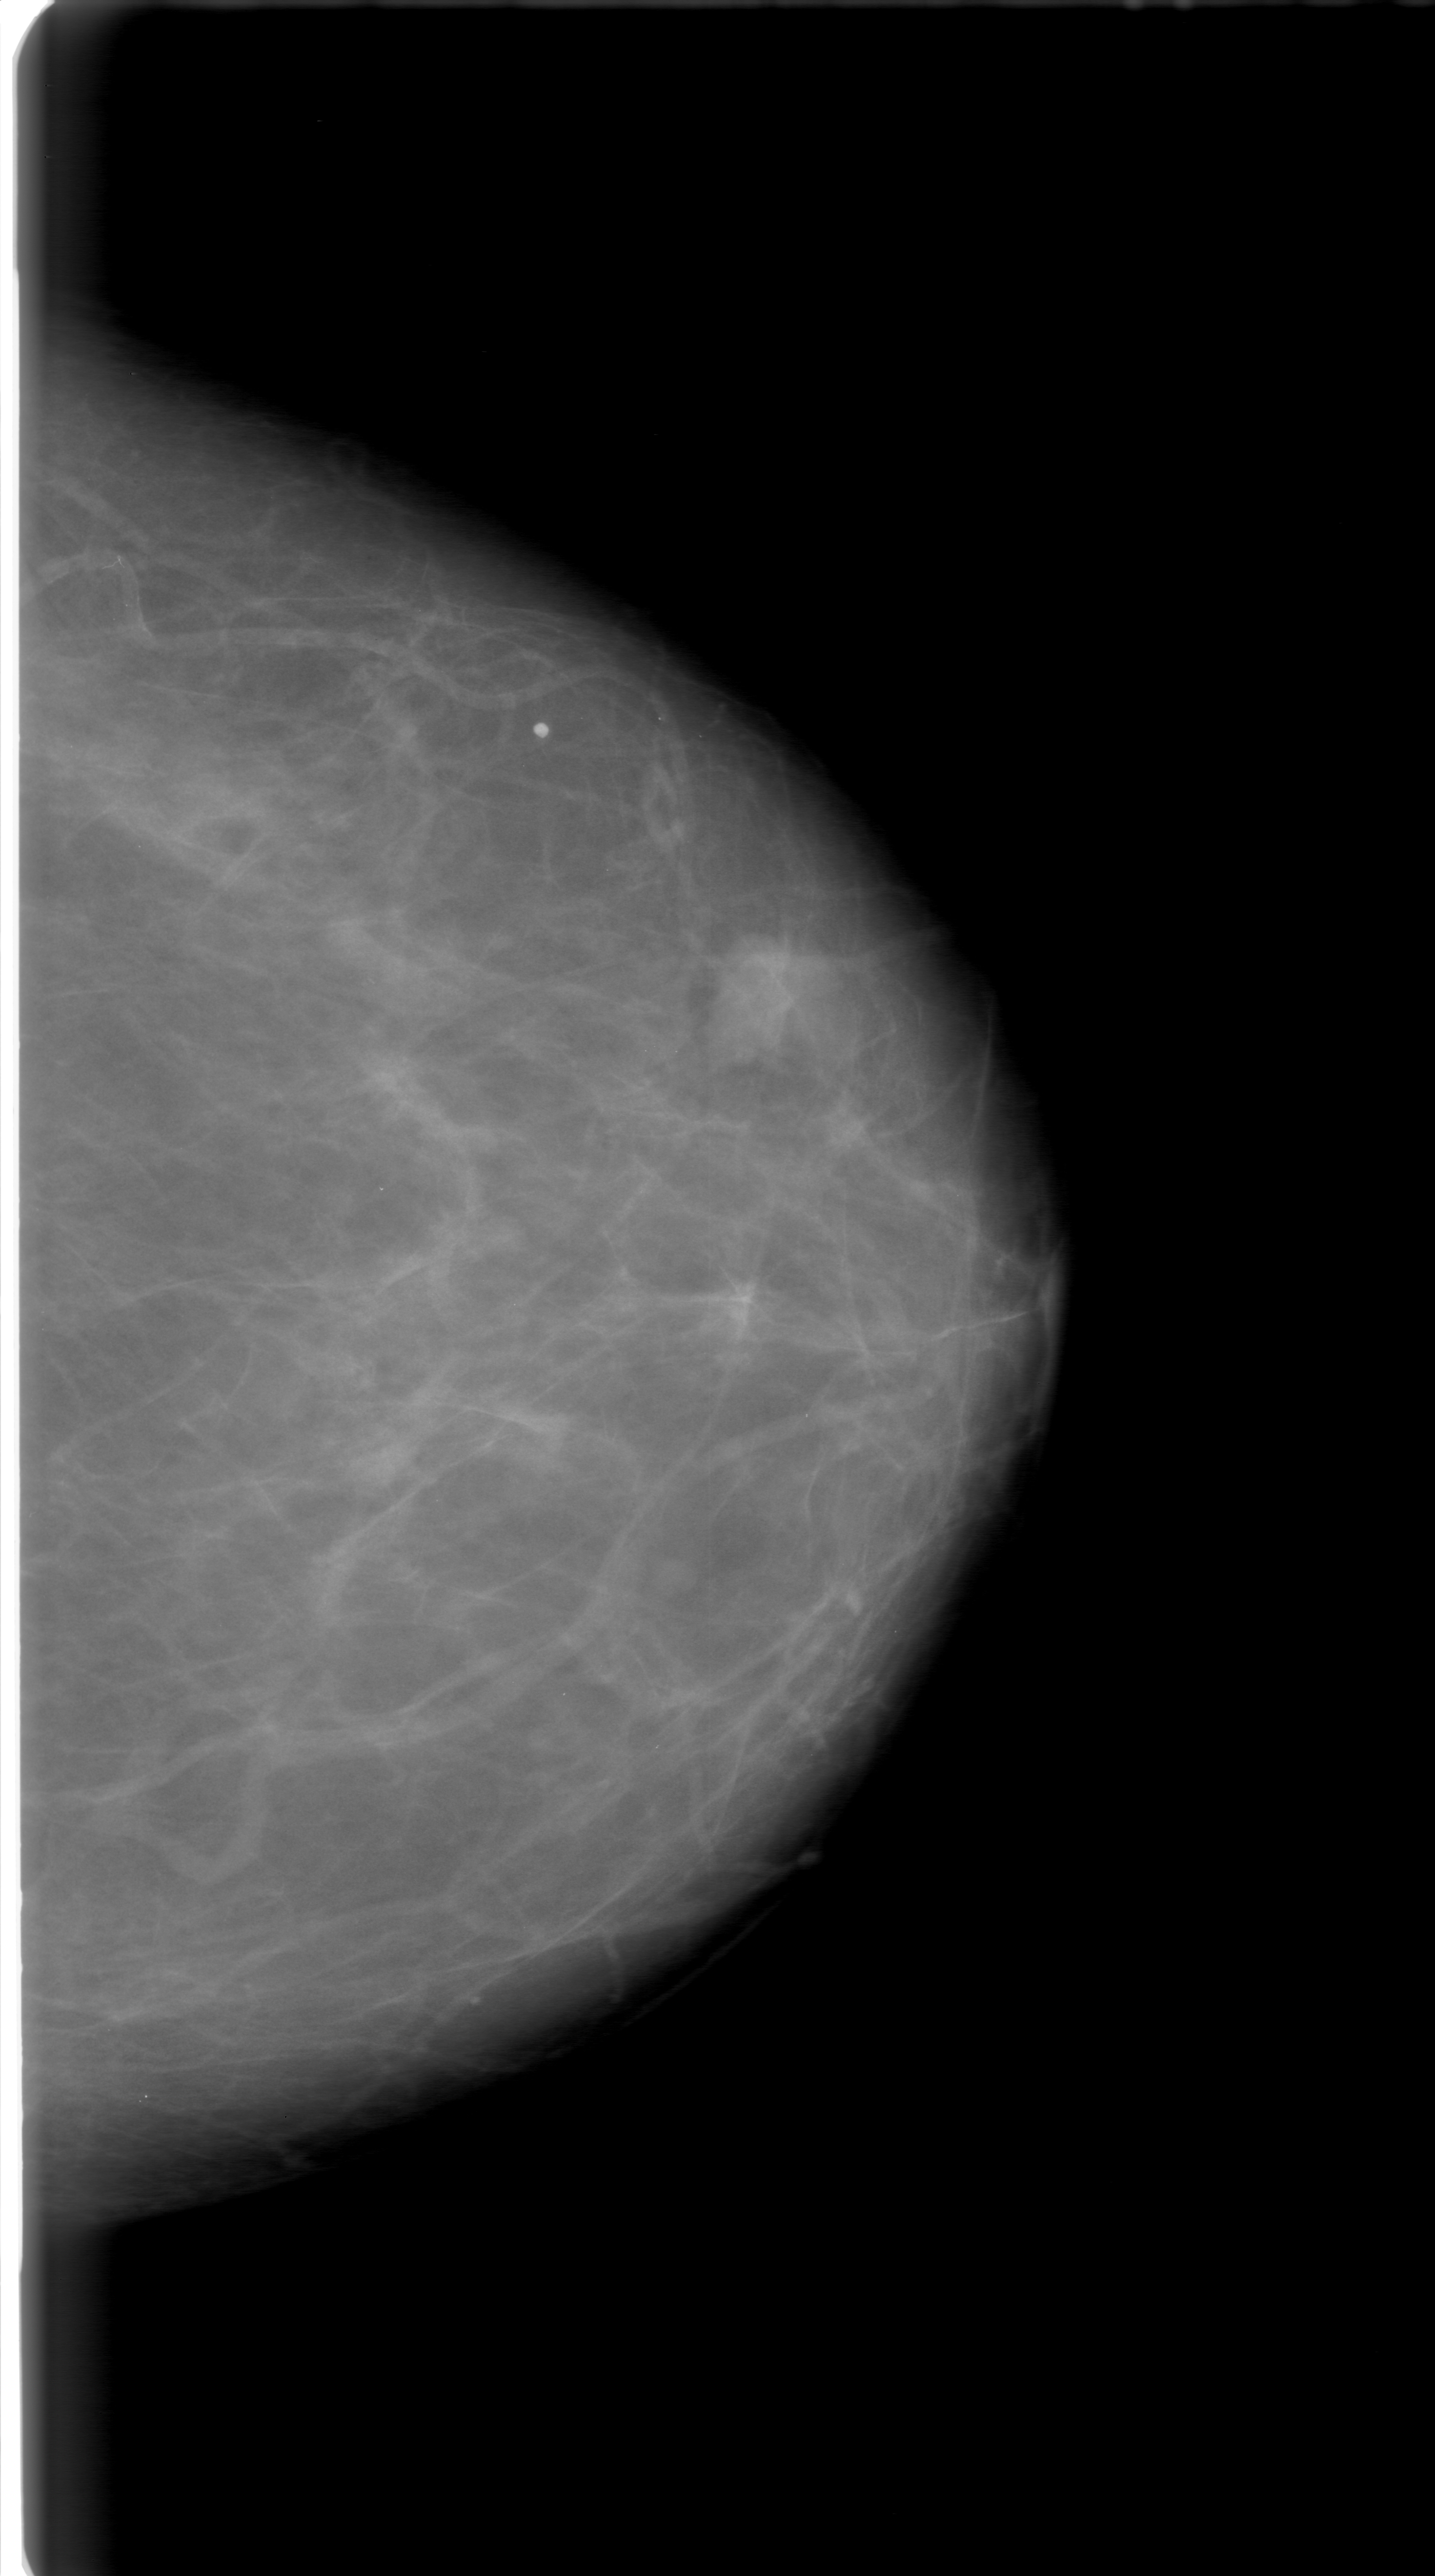
Digitized screen-film mammogram, left breast, craniocaudal (CC) view.
- Finding: mass, shape lobulated, margins obscured; BI-RADS assessment category 0; pathology (as recorded): benign.